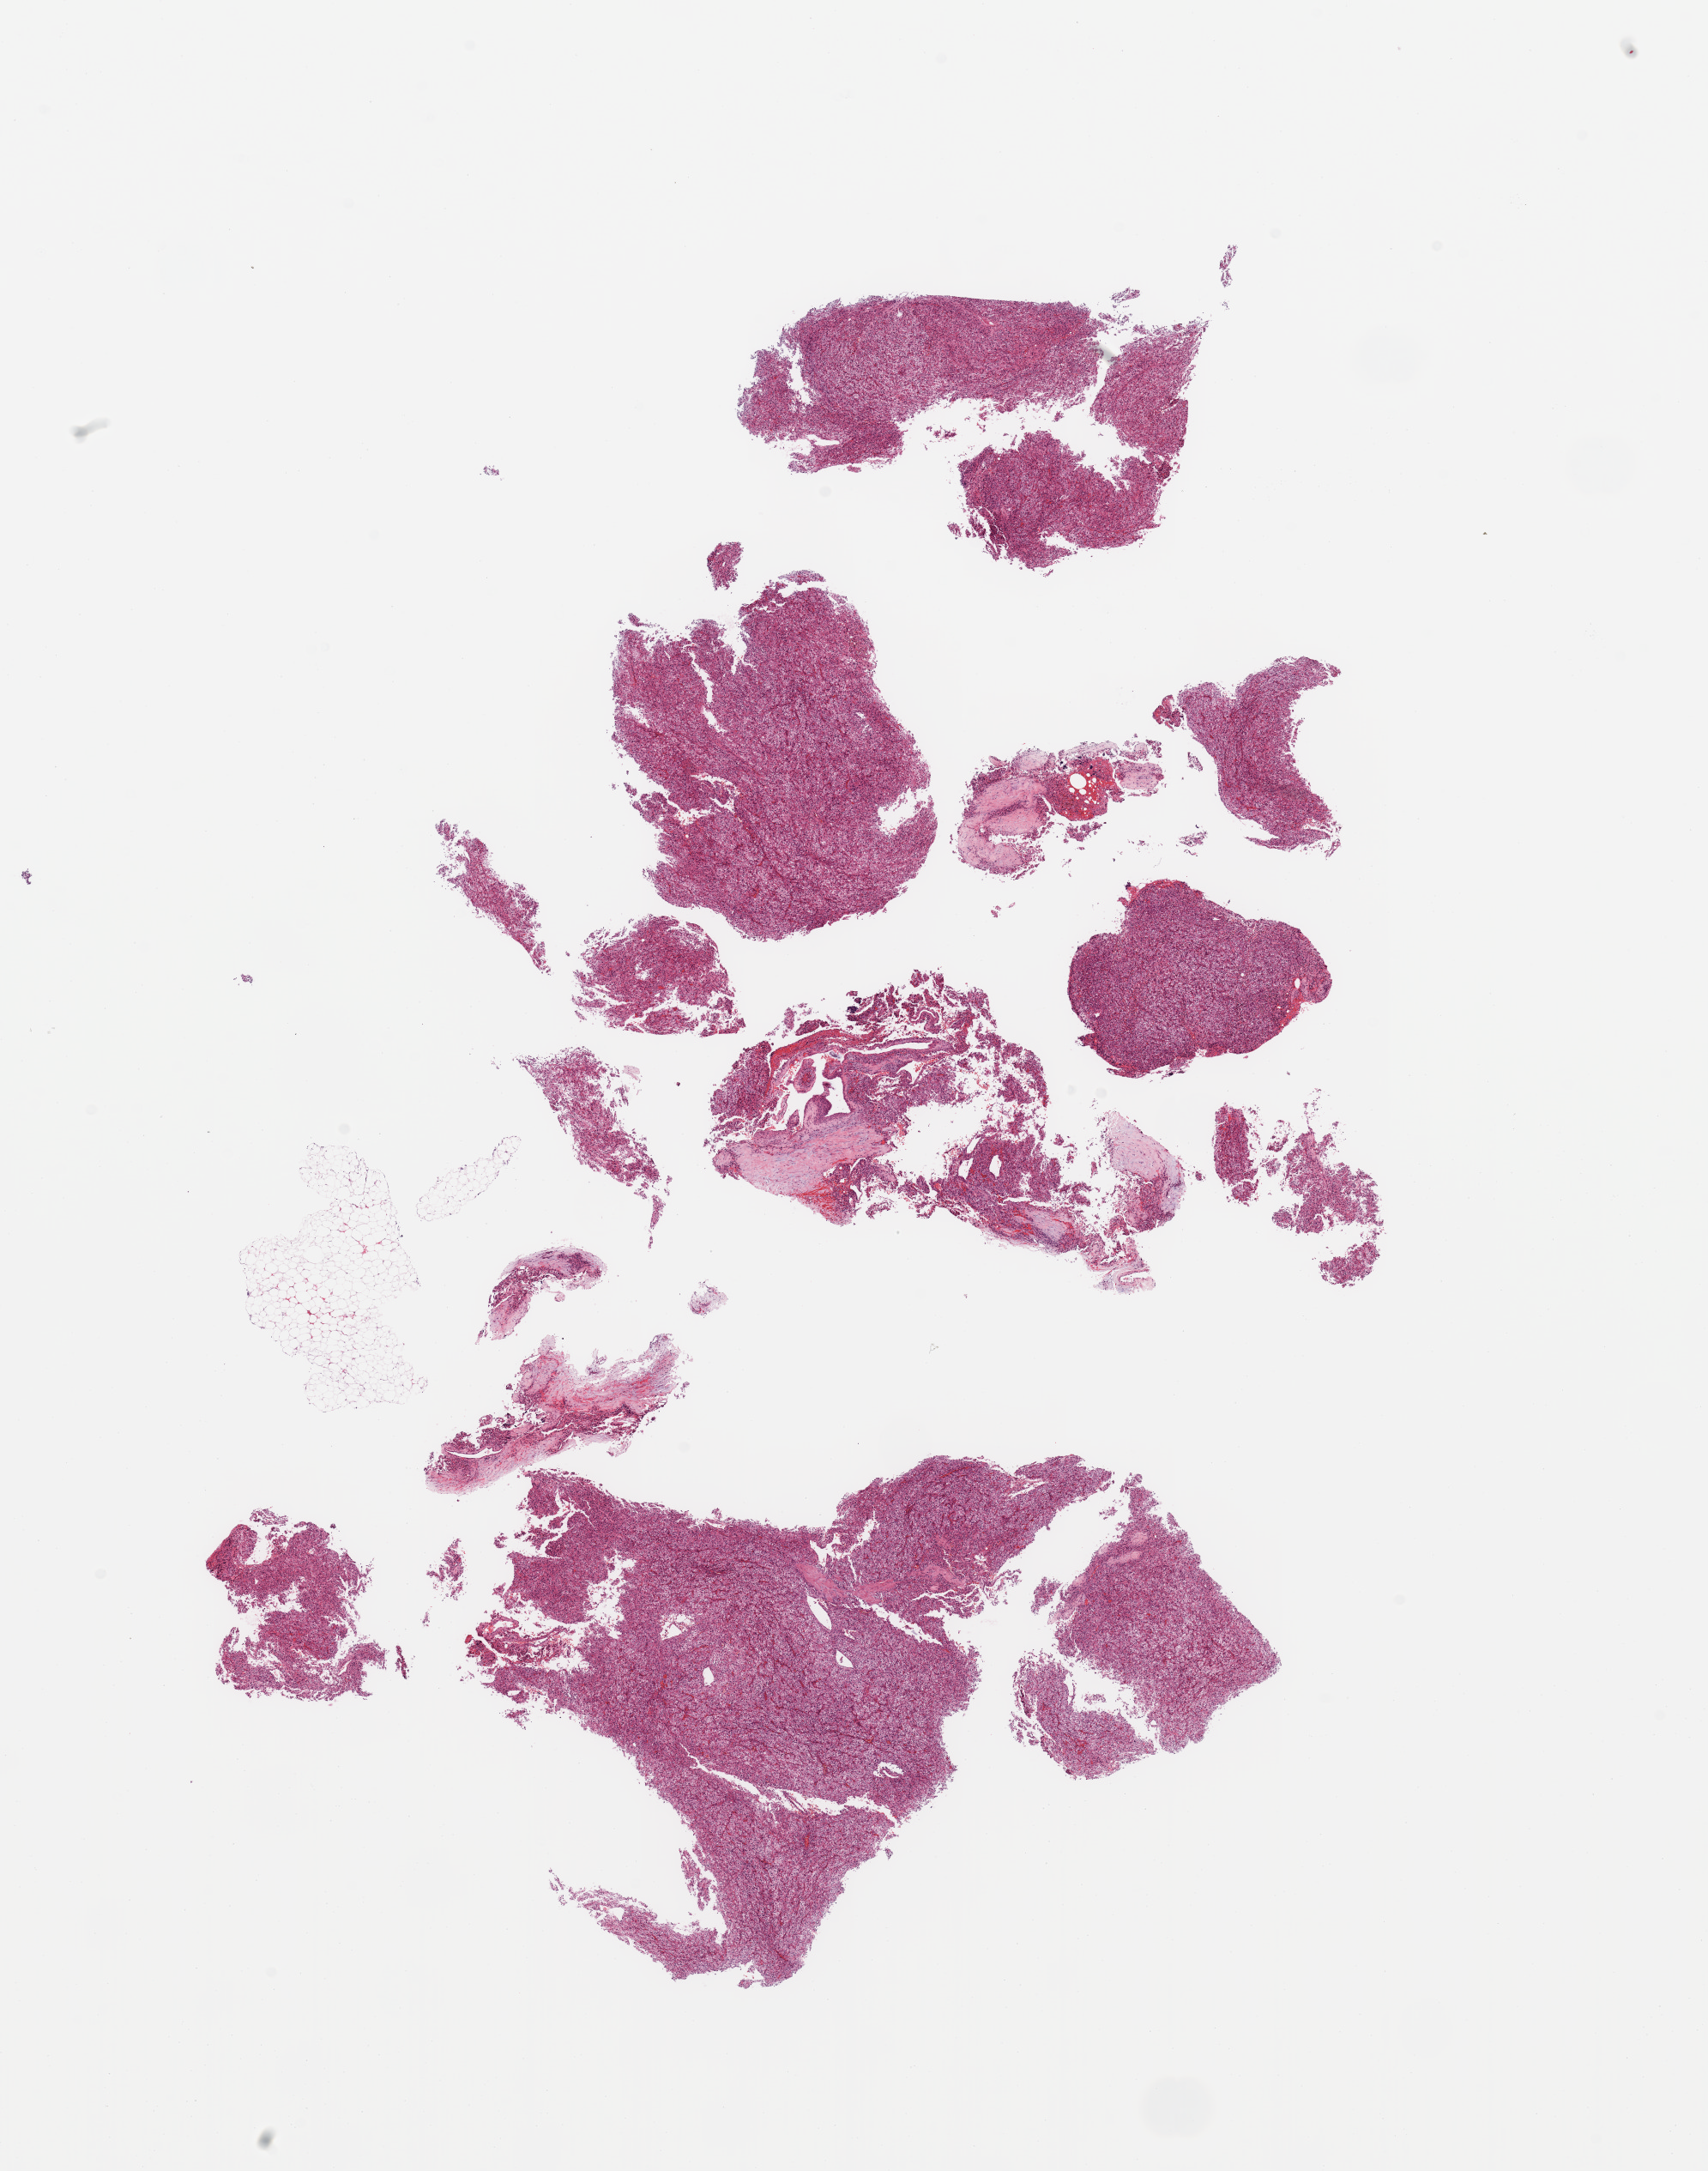
H&E whole-slide image — whole scanned area (about 15.8 x 20.0 mm) shown as a low-resolution overview. Tumour tissue sample, sampled site: kidney. Male, 58 y/o. Histologic grade: G3 (poorly differentiated). Composition of this section per pathologist review: tumour nuclei 80%, necrosis 5%.
* histologic diagnosis: Renal cell carcinoma, NOS
* AJCC pathologic stage: III